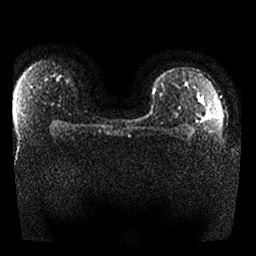
Breast MRI, one axial slice. Position 20 of 25 along the scan axis. Diffusion-weighted series; image 2 of 4 stored at this slice position (different b-values; order by instance number). 1.5 T. 4 mm slice thickness. 256 × 256 image matrix, field of view 330 × 330 mm. Female patient.
Annotated regions visible in this slice (manually delineated by an expert):
- tumour on diffusion-weighted imaging: bounding box [x1, y1, x2, y2] px = [197, 98, 211, 118]